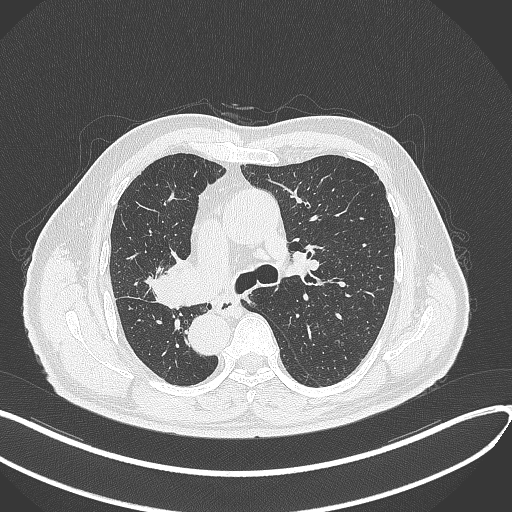
Chest CT, one axial slice; slice 191 of 300 in the series (ordered by position); reconstruction kernel B70f; lung window (W 1500 / L -600 HU); 1 mm slice thickness; 512 × 512 image matrix, field of view 400 × 400 mm. Patient: male, 67 years. From the clinical record (not read from this slice): clinical TNM (as recorded): T2a N0 M0.
Outlined on this slice (bounding box drawn by a radiologist):
- lung tumour (recorded histology: squamous cell carcinoma): bounding box <145,252,208,311> (left, top, right, bottom; pixels)